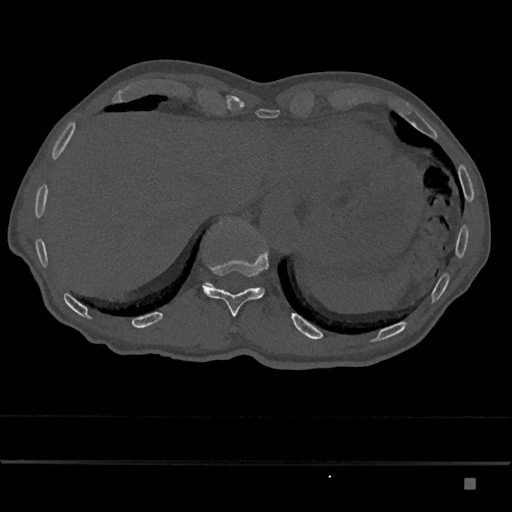
CT including the spine, one axial slice. 120 kVp. Bone window (W 1800 / L 400 HU). 0.5 mm slice thickness. 512 × 512 image matrix, field of view 390 × 390 mm. Male patient, age 72 years. From the clinical record (not read from this slice): primary cancer: prostate.
Structures marked on this image (semi-automatically segmented with operator editing):
- T11 vertebra: bounding box (x1, y1, x2, y2) in pixels: (202, 252, 269, 317)
- T12 vertebra: (204, 217, 249, 287)